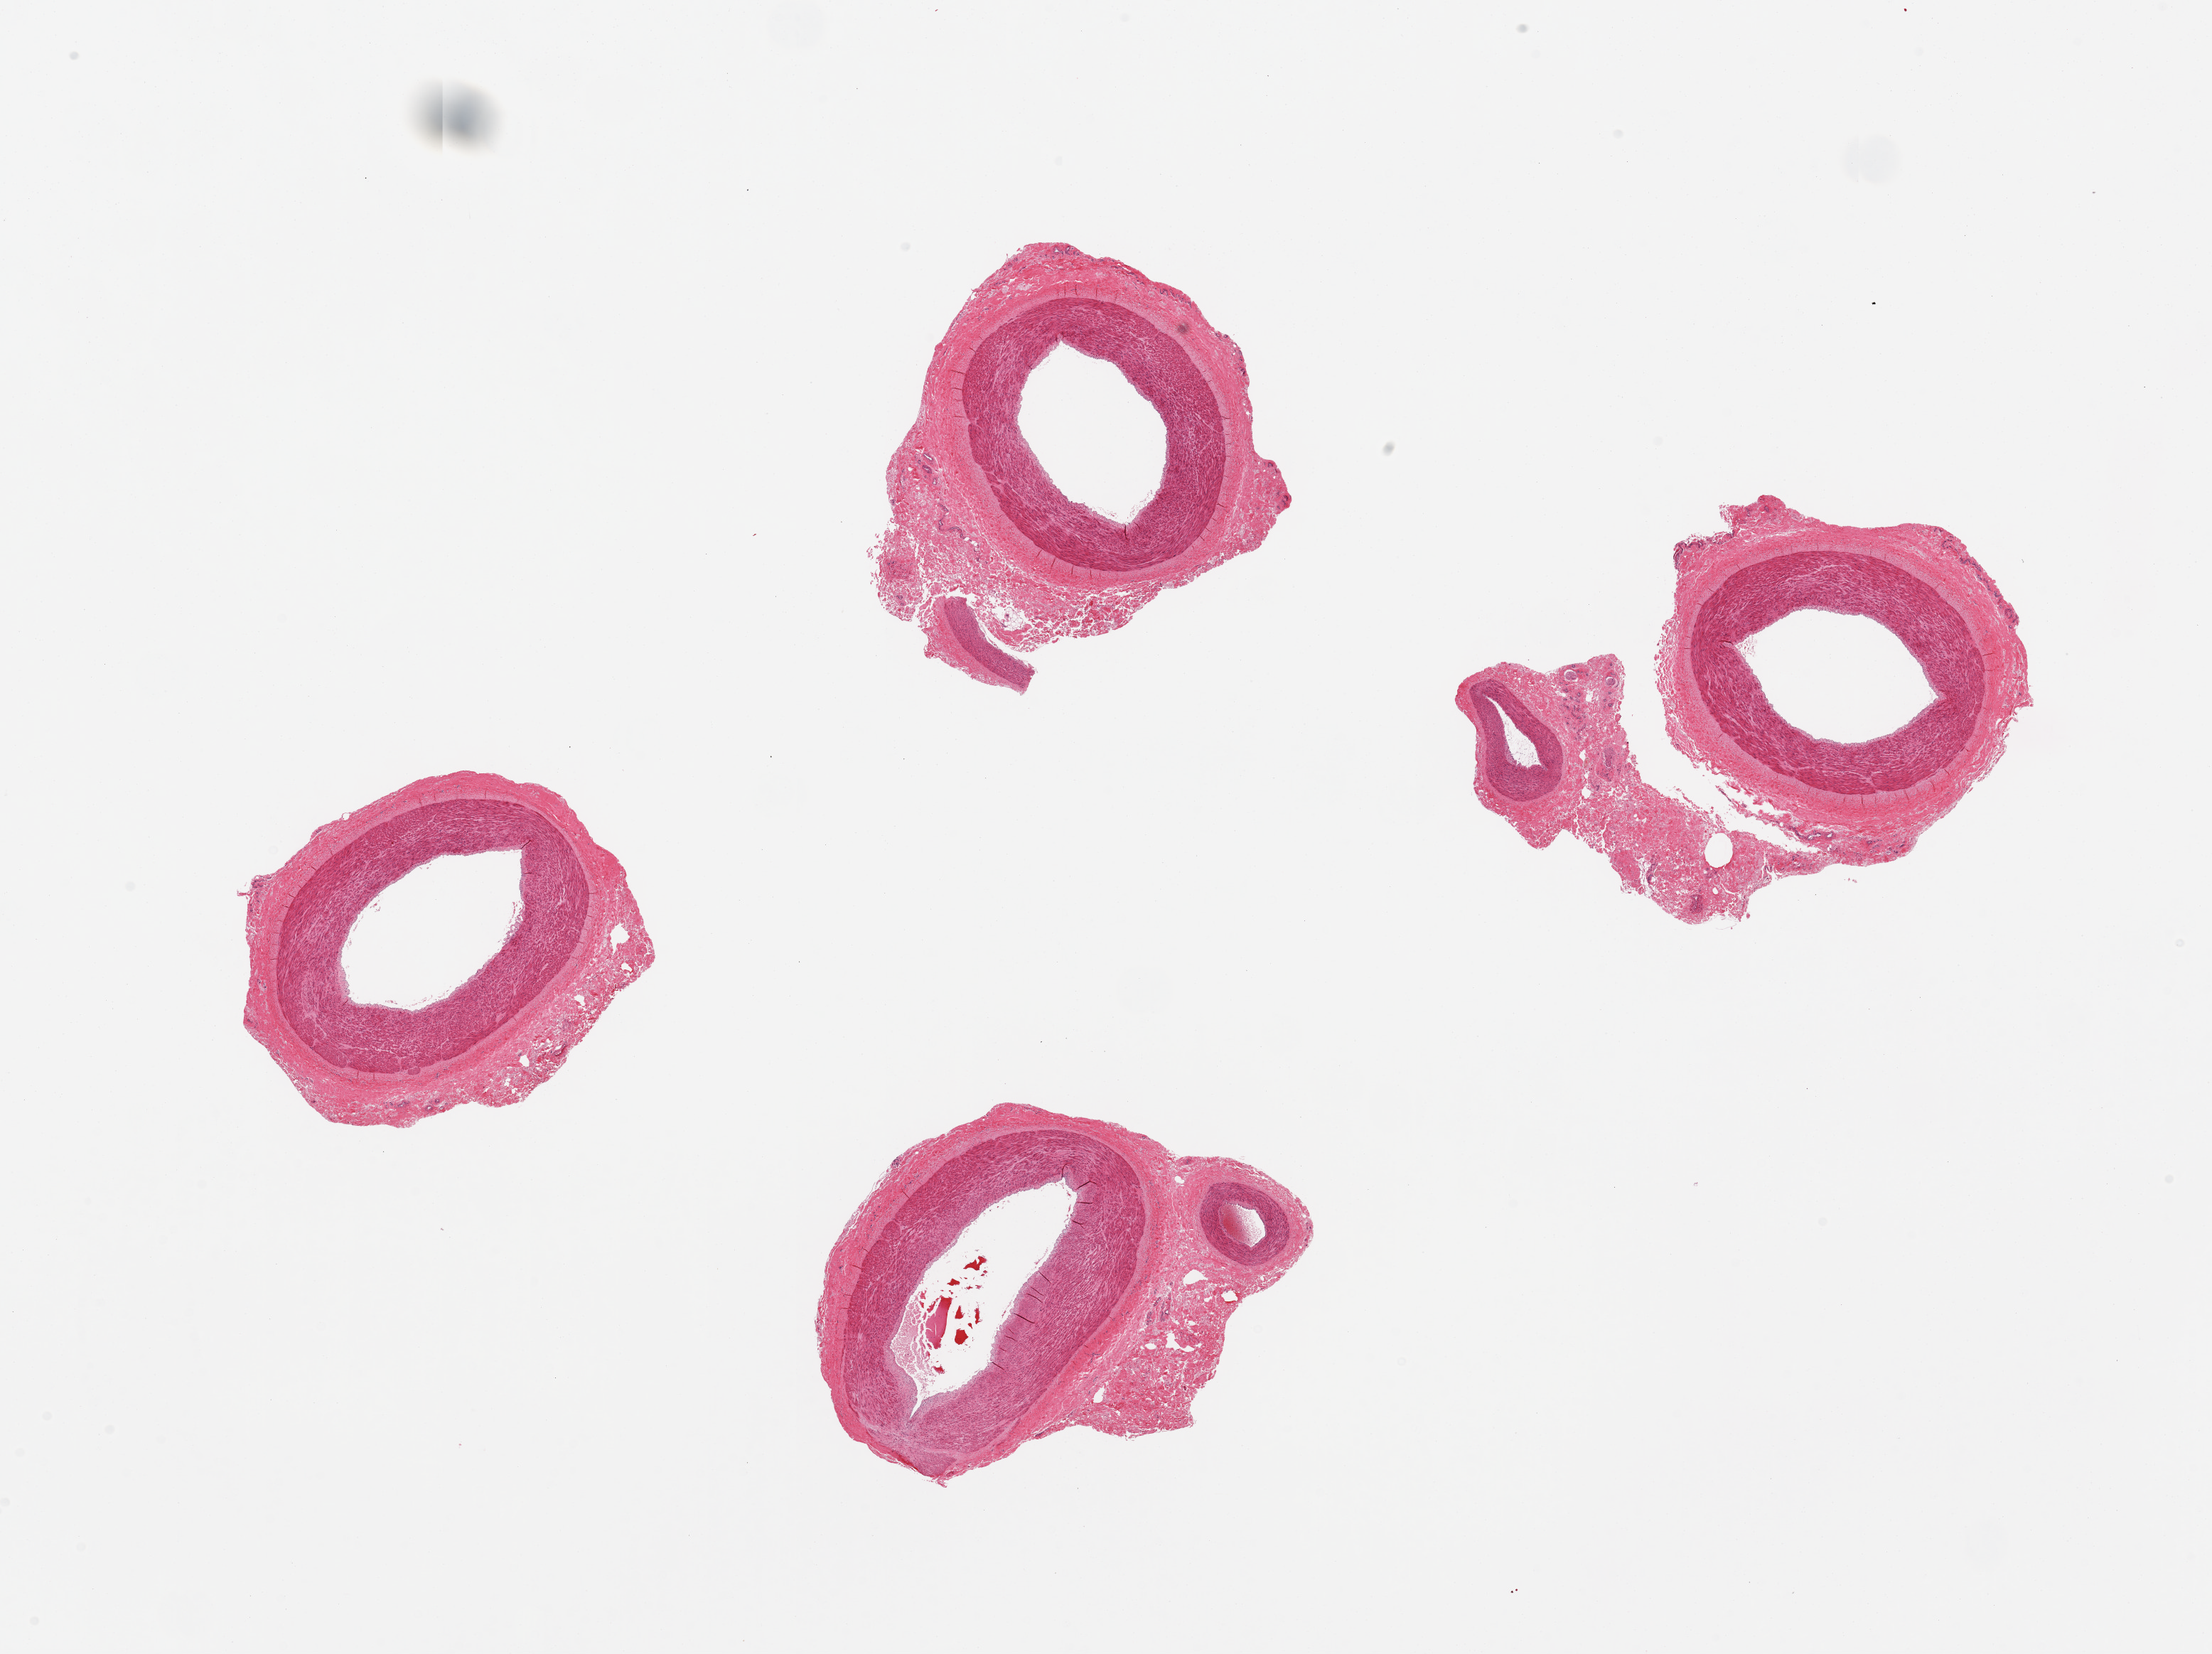
Hematoxylin and eosin (H&E) whole-slide image, shown as a low-resolution overview of the whole scanned area (about 24.6 x 18.4 mm), PAXgene-fixed, paraffin-embedded tissue, section of tibial artery (target tissue), donor tissue sample. Male donor.
Review note (as recorded): 4 pieces, up to 1mm adherent nubbins of fibrous tissue.